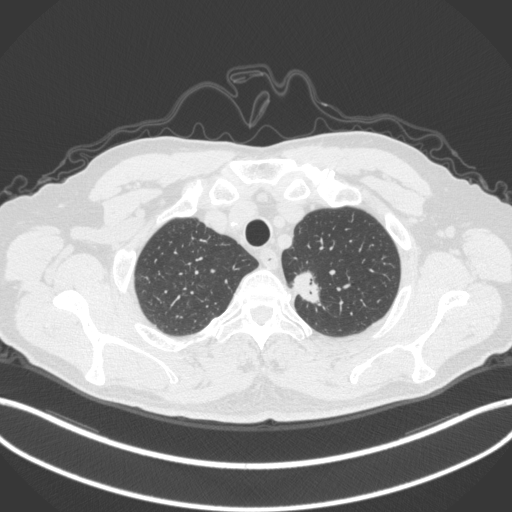
Chest CT, one axial slice; position 327 of 382 along the scan axis; lung window (W 1500 / L -600 HU); 512 × 512 image matrix, field of view 400 × 400 mm. Patient: male, 64 years. Case-level facts recorded for this patient, not image findings: clinical TNM (as recorded): T1c N0 M0.
Structures marked on this image (bounding box drawn by a radiologist):
- lung tumour (recorded histology: adenocarcinoma): bounding box <287,264,324,310> (left, top, right, bottom; pixels)